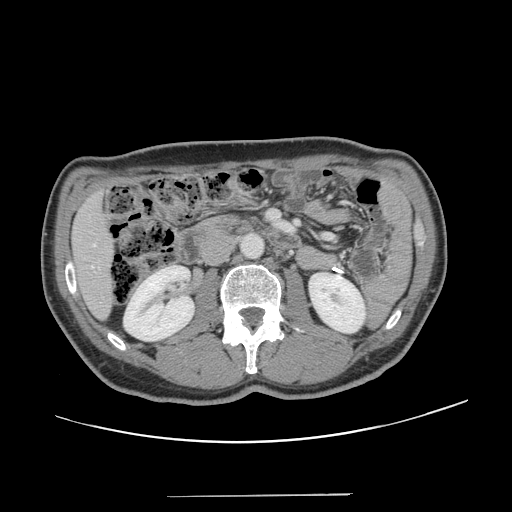
Contrast-enhanced abdominal CT, one axial slice. Position 53 of 131 along the scan axis. 120 kVp. Intravenous contrast given. Soft-tissue window (W 400 / L 40 HU). 2.5 mm slice thickness. 512 × 512 image matrix. Male patient, age 60 years. Case-level facts recorded for this patient, not image findings: diagnosis: colorectal cancer liver metastases, imaged before liver resection; multiple liver metastases: no; largest metastasis: 2.5 cm; chemotherapy before resection: no.
Outlined on this slice (outlined manually by an expert reader):
- hepatic veins: box from (x=92, y=244) to (x=96, y=268) px
- liver: (x=74, y=196)–(x=112, y=316)
- planned liver remnant (the part of the liver to remain after resection): (x=74, y=196)–(x=112, y=316)